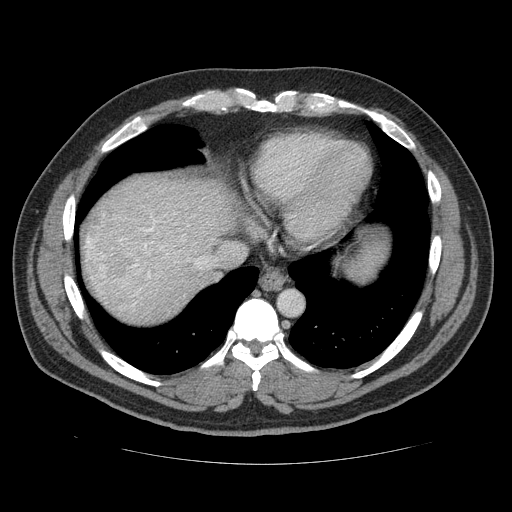
Contrast-enhanced abdominal CT (liver protocol), one axial slice; position 105 of 113 along the scan axis; reconstruction kernel STANDARD; 120 kVp; soft-tissue window (W 400 / L 40 HU); 2.5 mm slice thickness; 512 × 512 image matrix. From the clinical record (not read from this slice): diagnosis: hepatocellular carcinoma (patient treated with transarterial chemoembolisation; whether this scan precedes or follows treatment is not stated here); TNM stage (as recorded): Stage-II; Child-Pugh class: B; tumour differentiation: moderately differentiated; tumour nodularity: multinodular.
Outlined on this slice (semi-automatically segmented with operator editing):
- abdominal aorta: bounding box <279,292,302,315> (left, top, right, bottom; pixels)
- liver parenchyma outside the tumour (the mass and vessels are separate outlines, so this box may not span the whole liver): <82,172,226,318>
- mass: <110,250,131,273>
- liver vessels: <129,226,154,283>